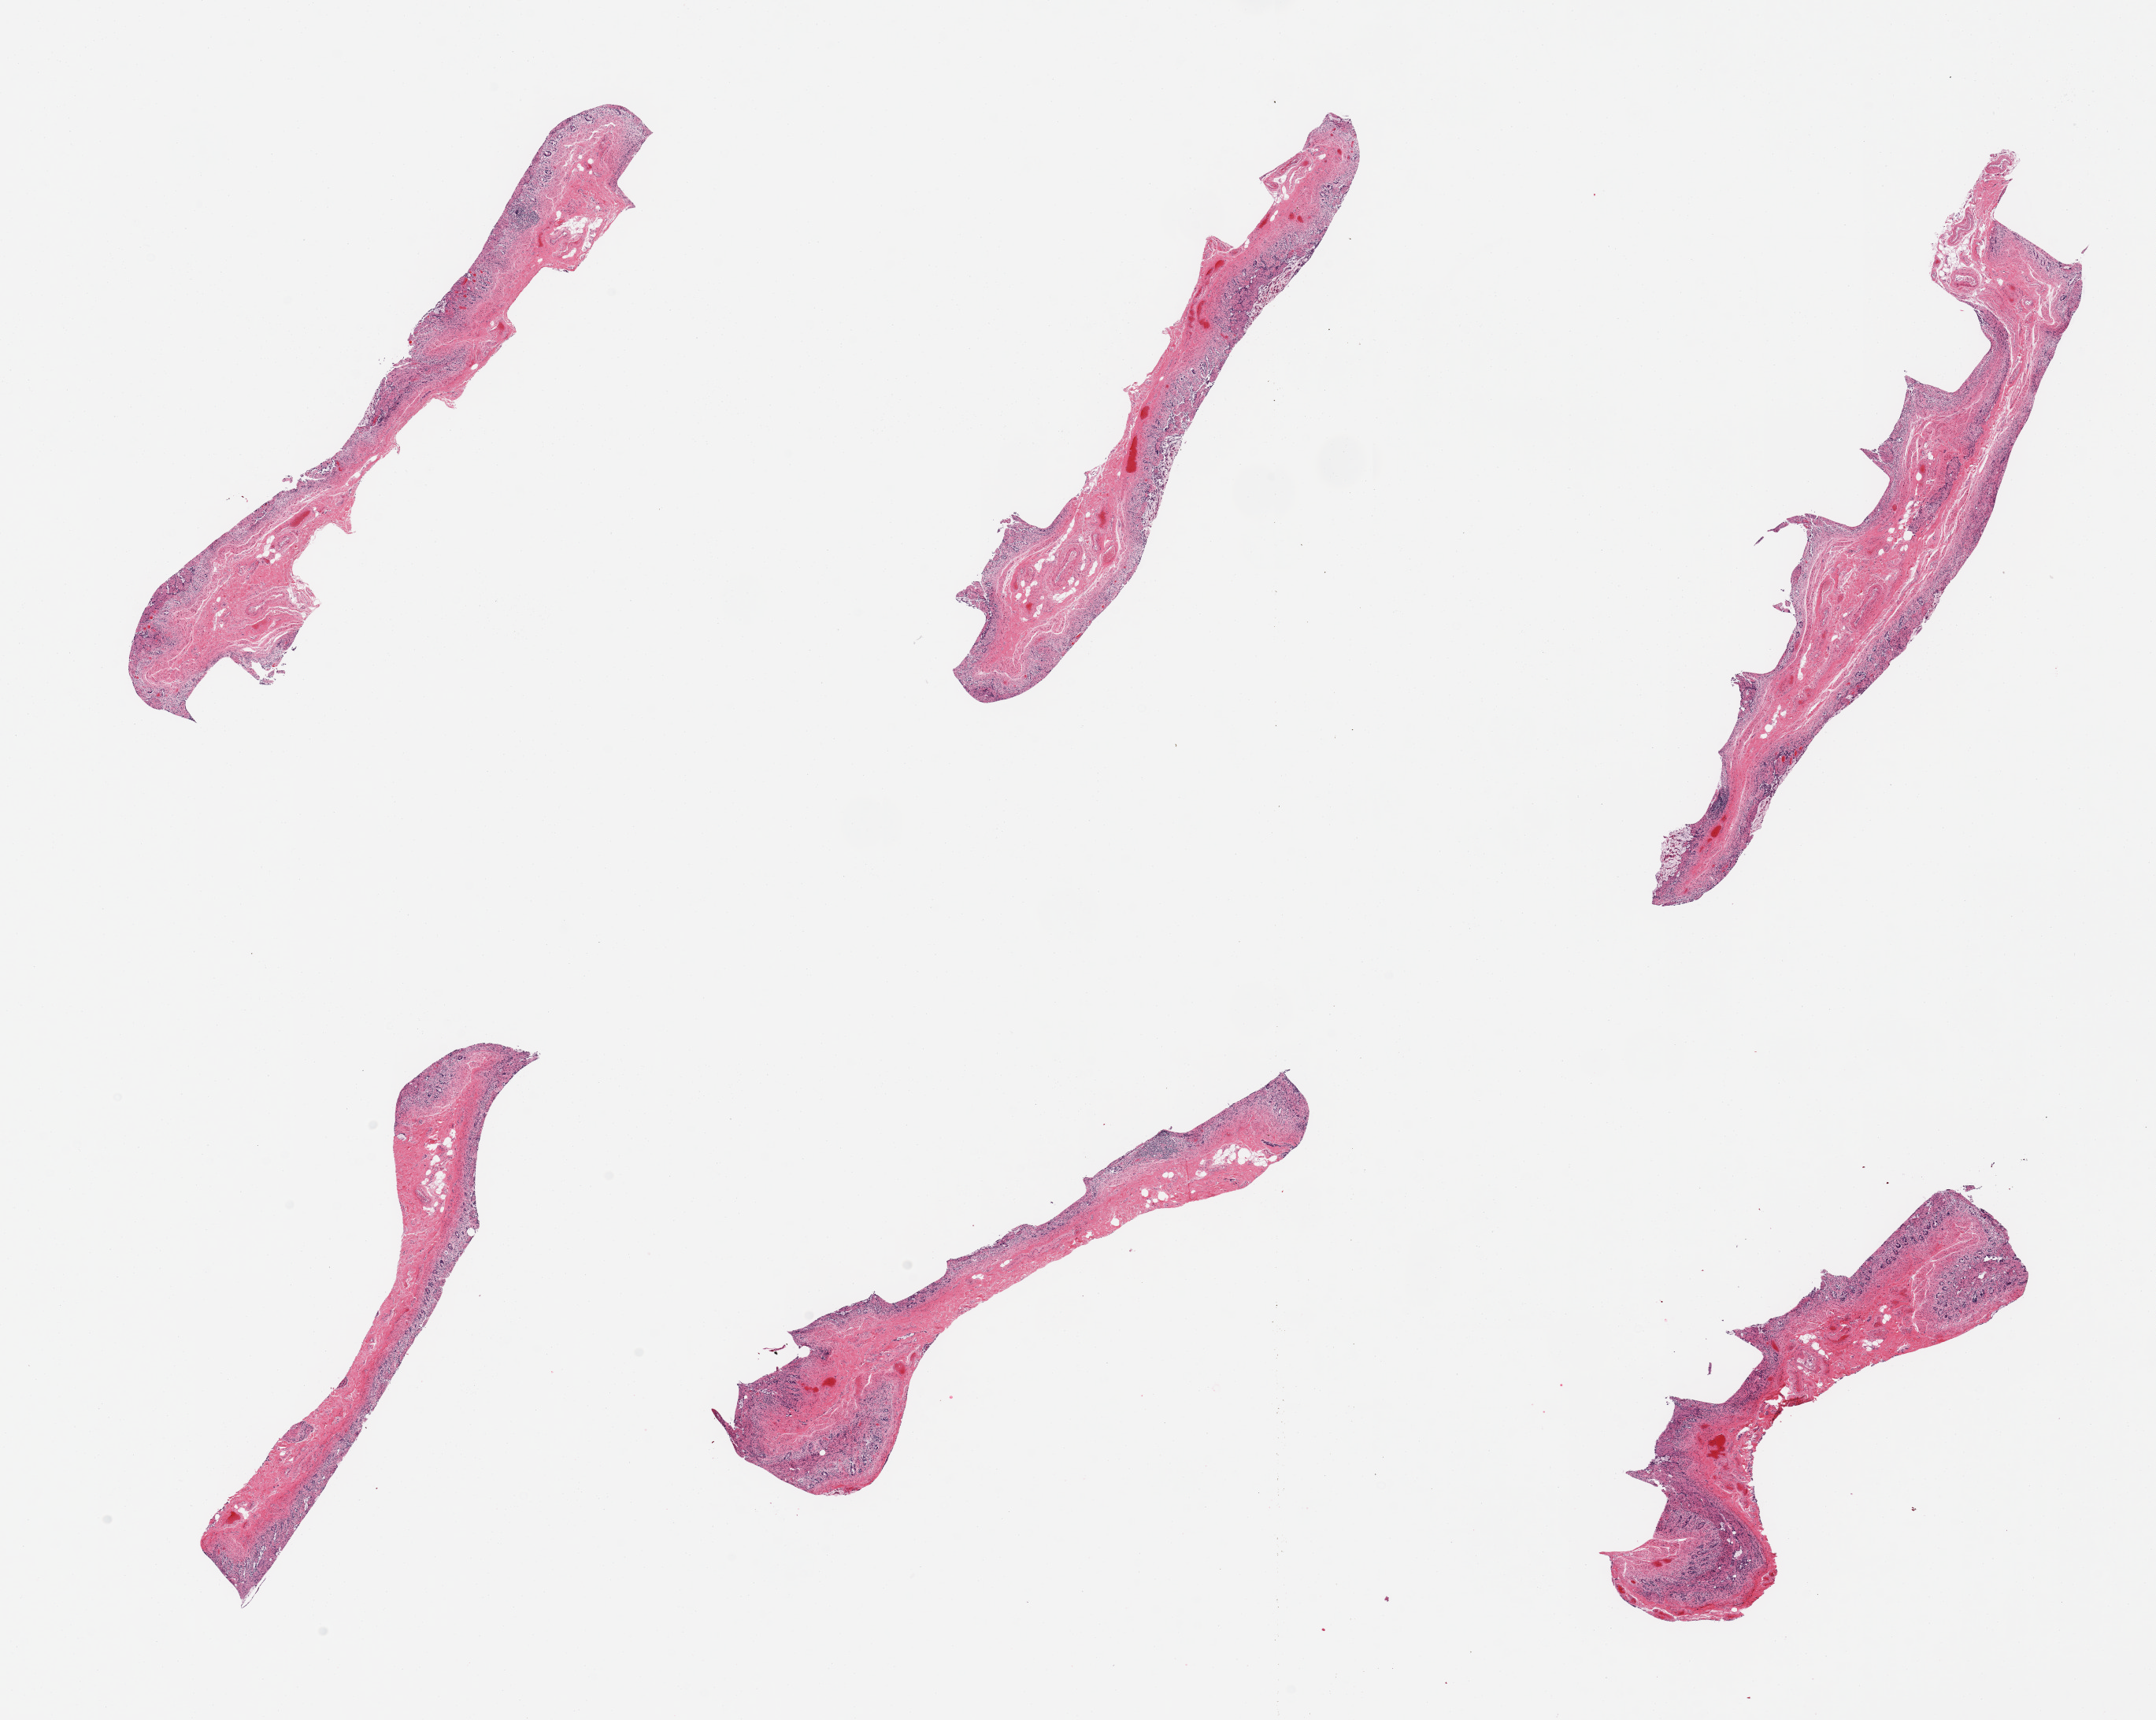
H&E whole-slide image — low-resolution overview of the scanned area, about 21.7 x 17.3 mm, PAXgene-fixed, paraffin-embedded tissue, sampled site (target tissue): ileum, tissue donor sample. Male donor.
* reviewer comment on this tissue sample: 6 pieces; no lymphoid nodules present